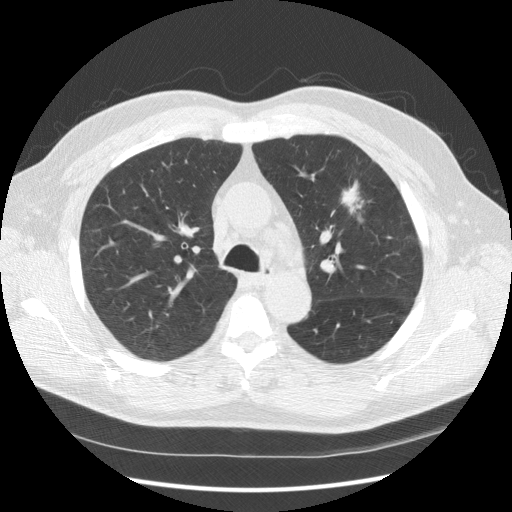
Axial slice from a low-dose chest CT screening exam; second screening round (one year after baseline); lung window (W 1500 / L -600 HU); 2.5 mm slice thickness; standard (soft-tissue) reconstruction kernel (STANDARD). Male, age 65 years at enrolment. Current smoker at enrolment.
Expert-annotated lung lesion, bounding box (x1, y1, x2, y2) in pixels: (326, 173, 376, 227). The screening reader recorded 2 non-calcified nodules or masses ≥4 mm on this exam (left upper lobe, right upper lobe); which of them this box marks is not recorded. Official screen result: positive, other. Participant outcome: lung cancer diagnosed 120 days after this screen — carcinoma, NOS, left upper lobe, poorly differentiated (G3), stage IIIA (AJCC 6th edition), 25 mm at pathology.